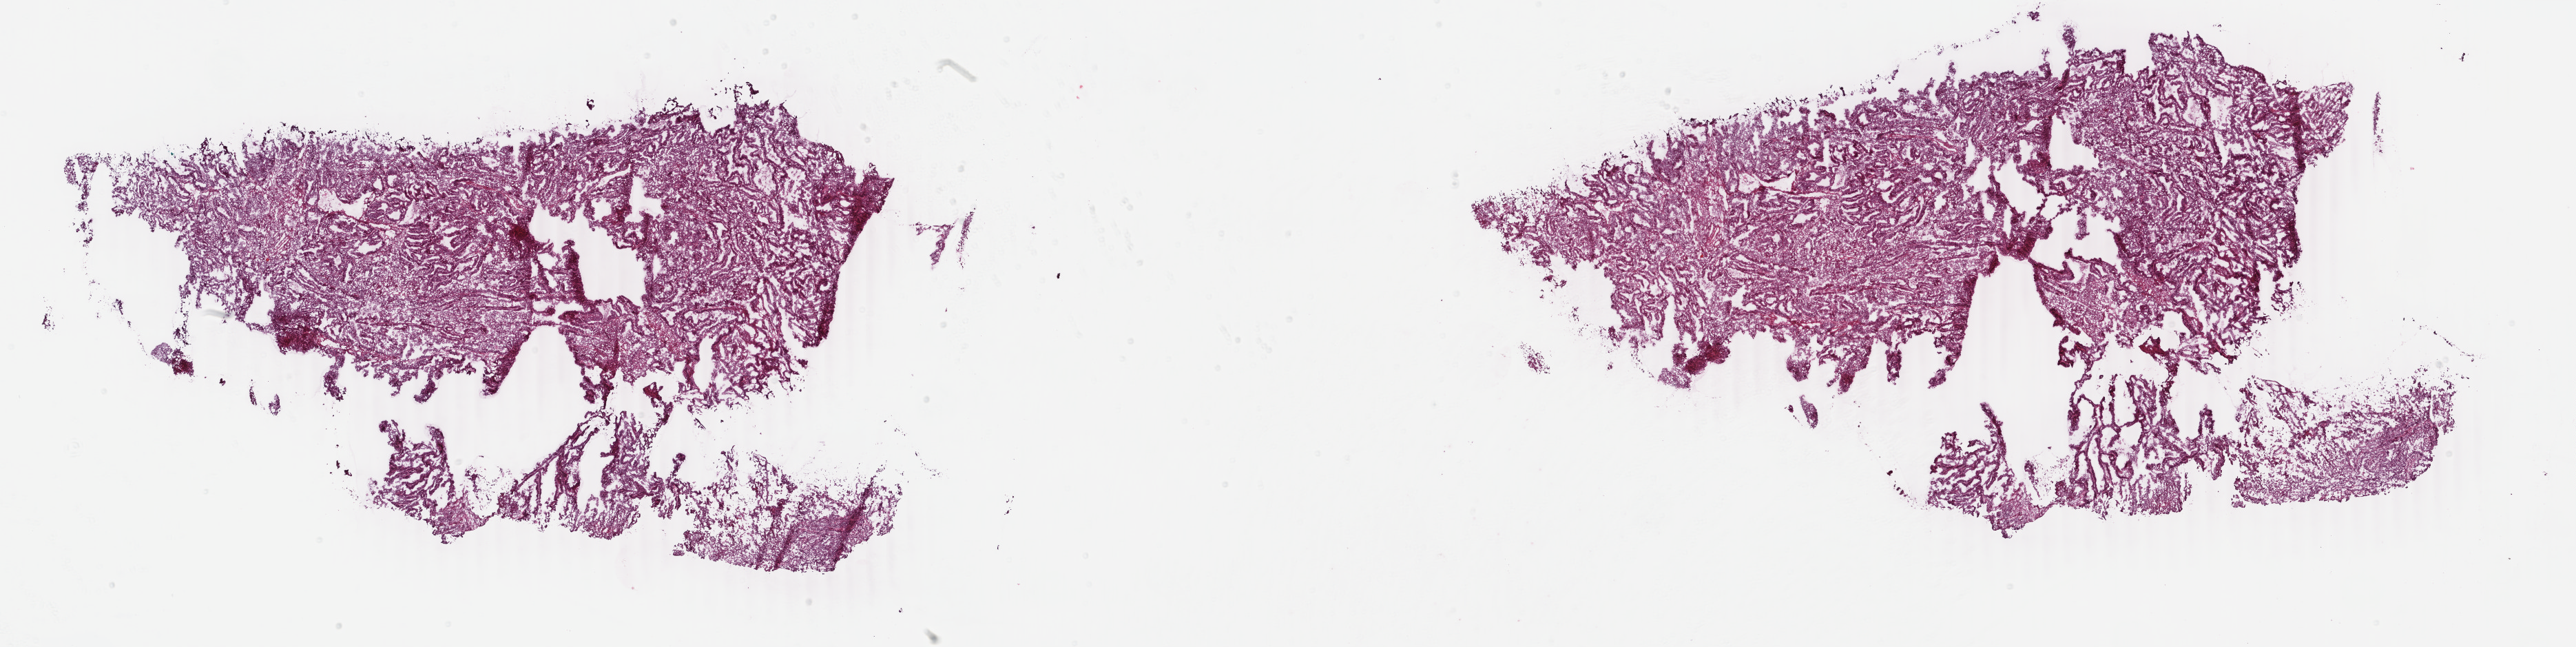
Whole-slide histology image, H&E-stained, low-resolution overview of the scanned area, about 29.7 x 7.5 mm (slide scanned at 40x). Frozen section from the bottom of the tissue portion. Primary tumour sample from the uterus. Female, age 82 years at initial diagnosis. Histologic grade: G1 (well differentiated). Slide review estimates, as recorded: tumour cells 83%, tumour nuclei 85%, normal cells 2%, stromal cells 5%, necrosis 10%. Infiltration values recorded for this section: lymphocyte infiltration 1%, monocyte infiltration 3%, neutrophil infiltration 1%.
- pathologic diagnosis: Endometrioid adenocarcinoma, NOS (endometrium)
- FIGO stage: IB